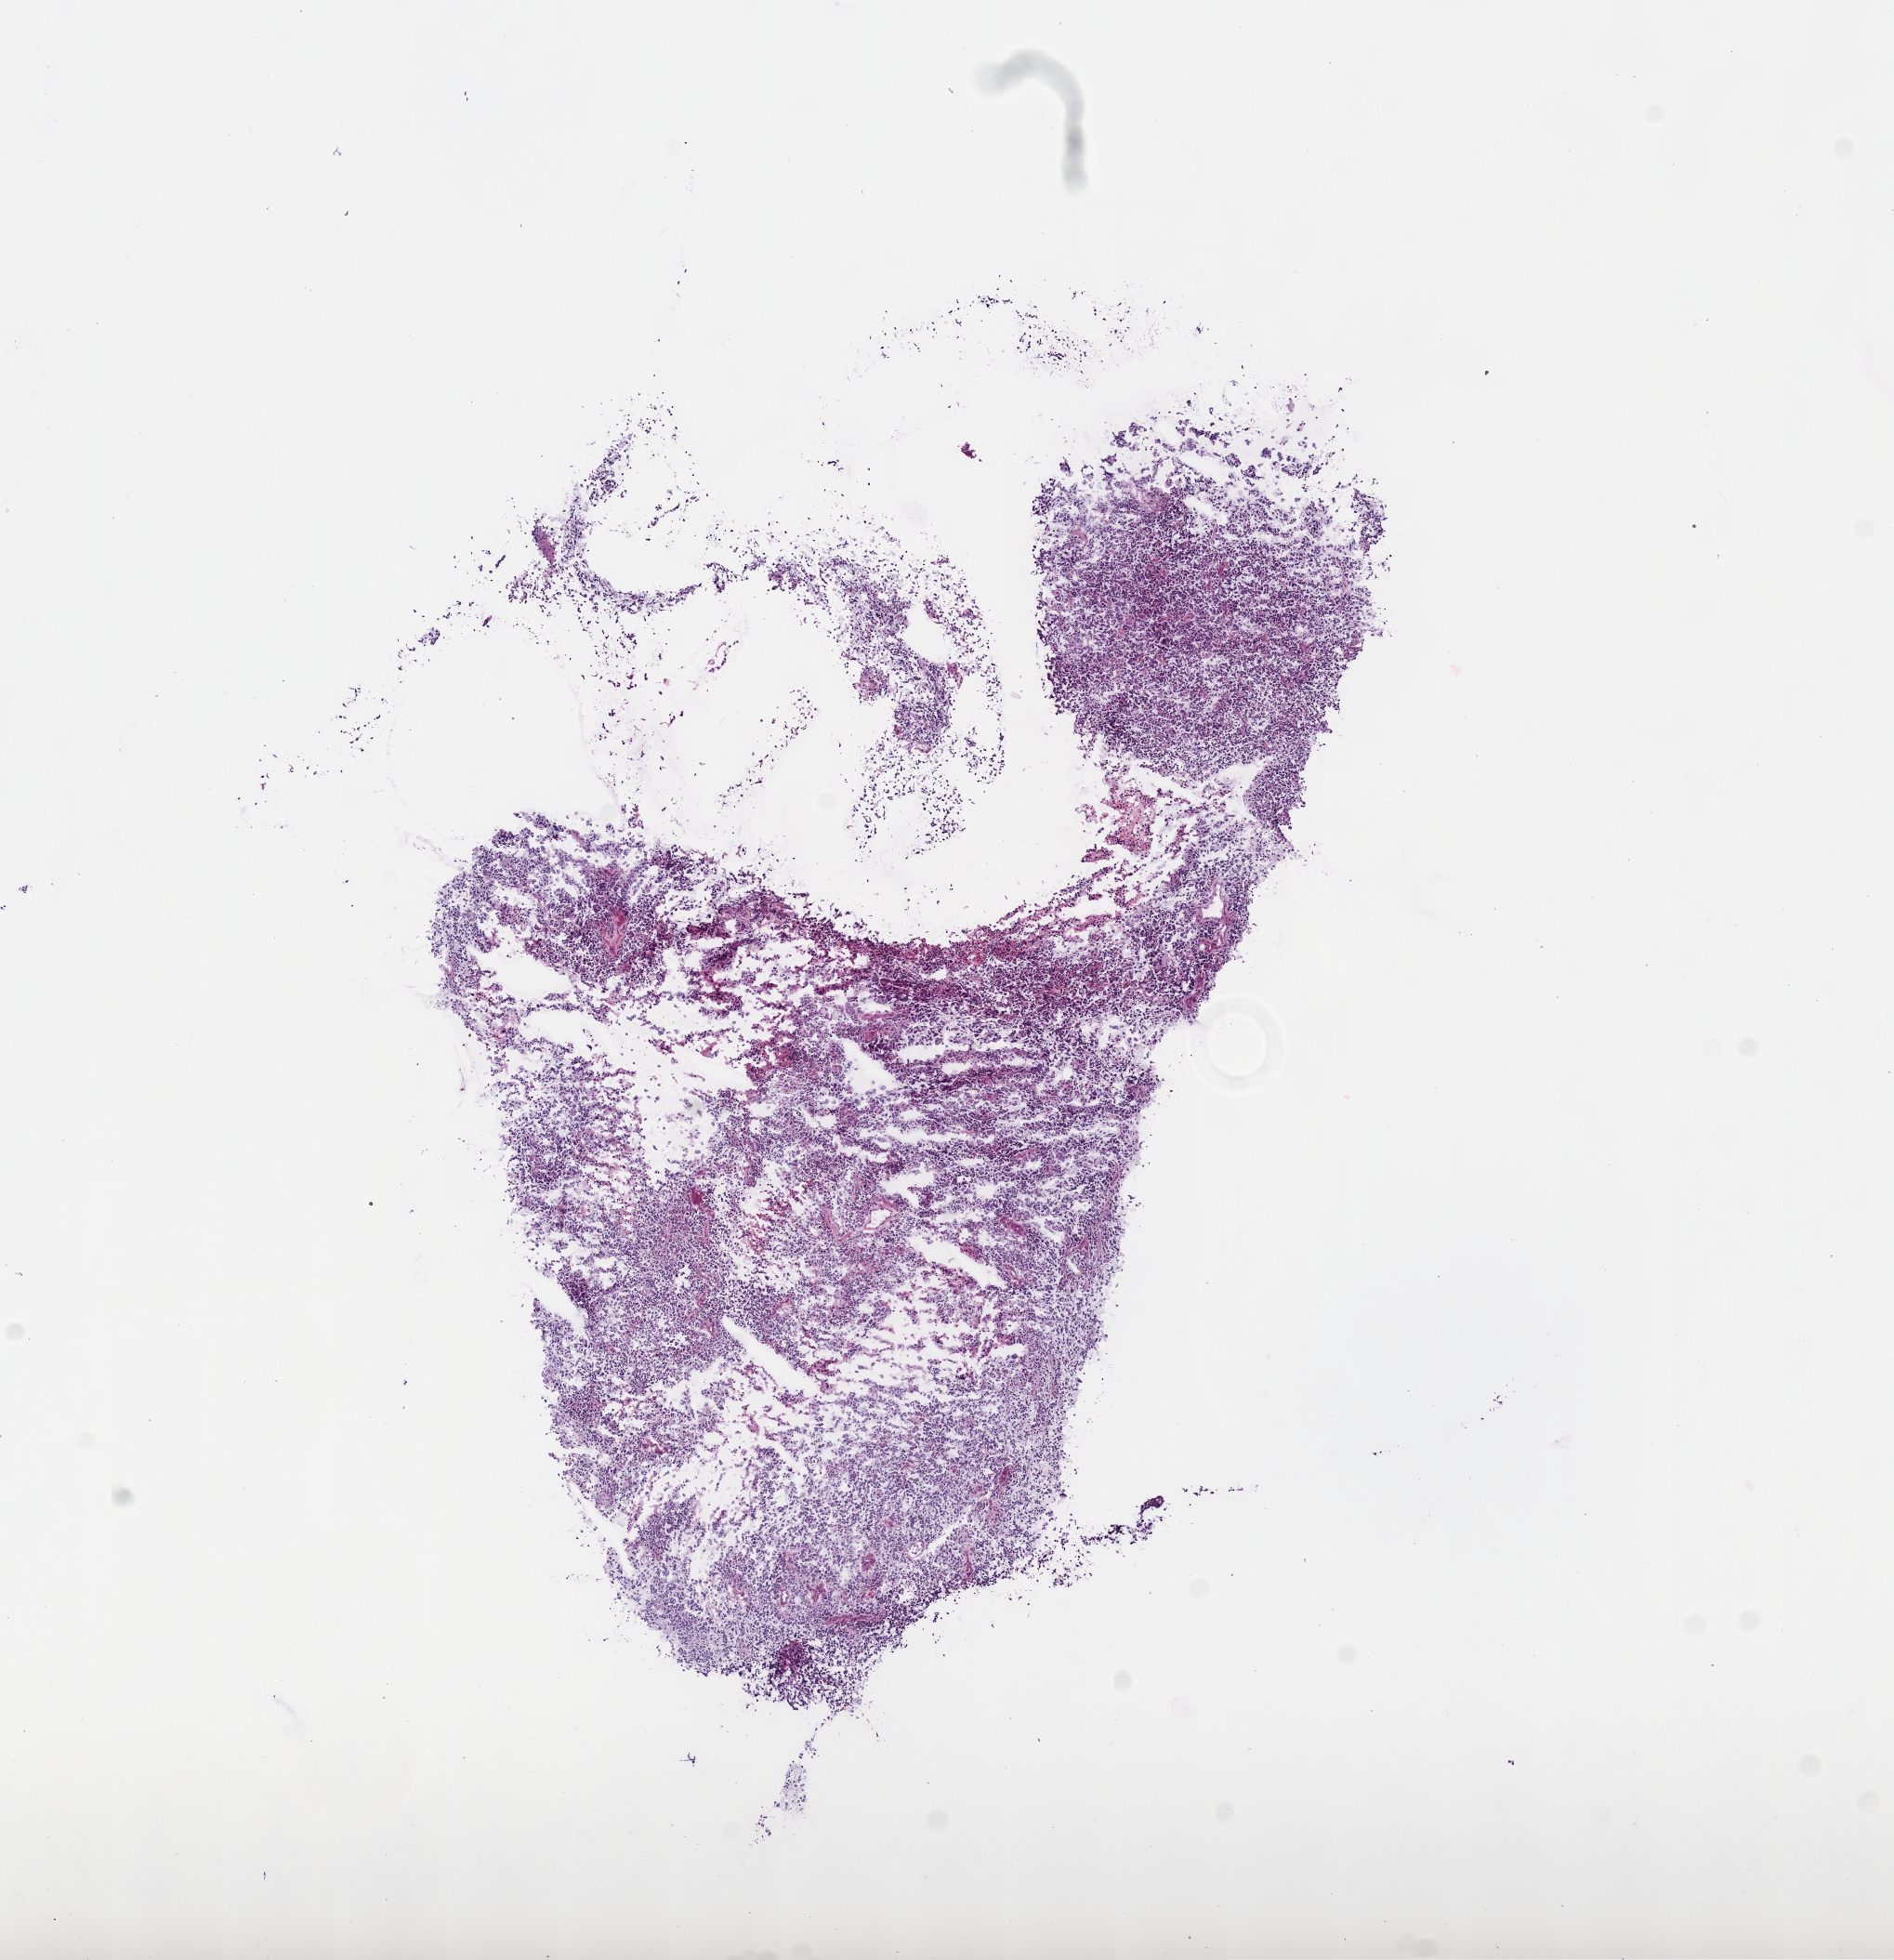
H&E-stained whole-slide image — low-resolution overview of the scanned area, about 8.2 x 8.5 mm (from a 20x scan), frozen section from the top of the tissue portion, brain, primary tumour sample. Female patient; age at initial diagnosis 52 years. Slide review estimates, as recorded: tumour cells 95%, tumour nuclei 98%, stromal cells 5%, necrosis 0%.
- pathologic diagnosis: Glioblastoma